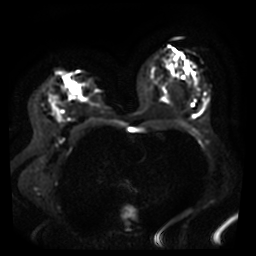
Breast MRI, one axial slice. Position 23 of 46 along the scan axis. Diffusion-weighted series; image 2 of 4 stored at this slice position (different b-values; order by instance number). 3 T. 5 mm slice thickness. 256 × 256 image matrix, field of view 360 × 360 mm. Female patient.
Outlined on this slice (expert manual segmentation):
- tumour on diffusion-weighted imaging: bounding box (x1, y1, x2, y2) in pixels: (52, 104, 62, 121)